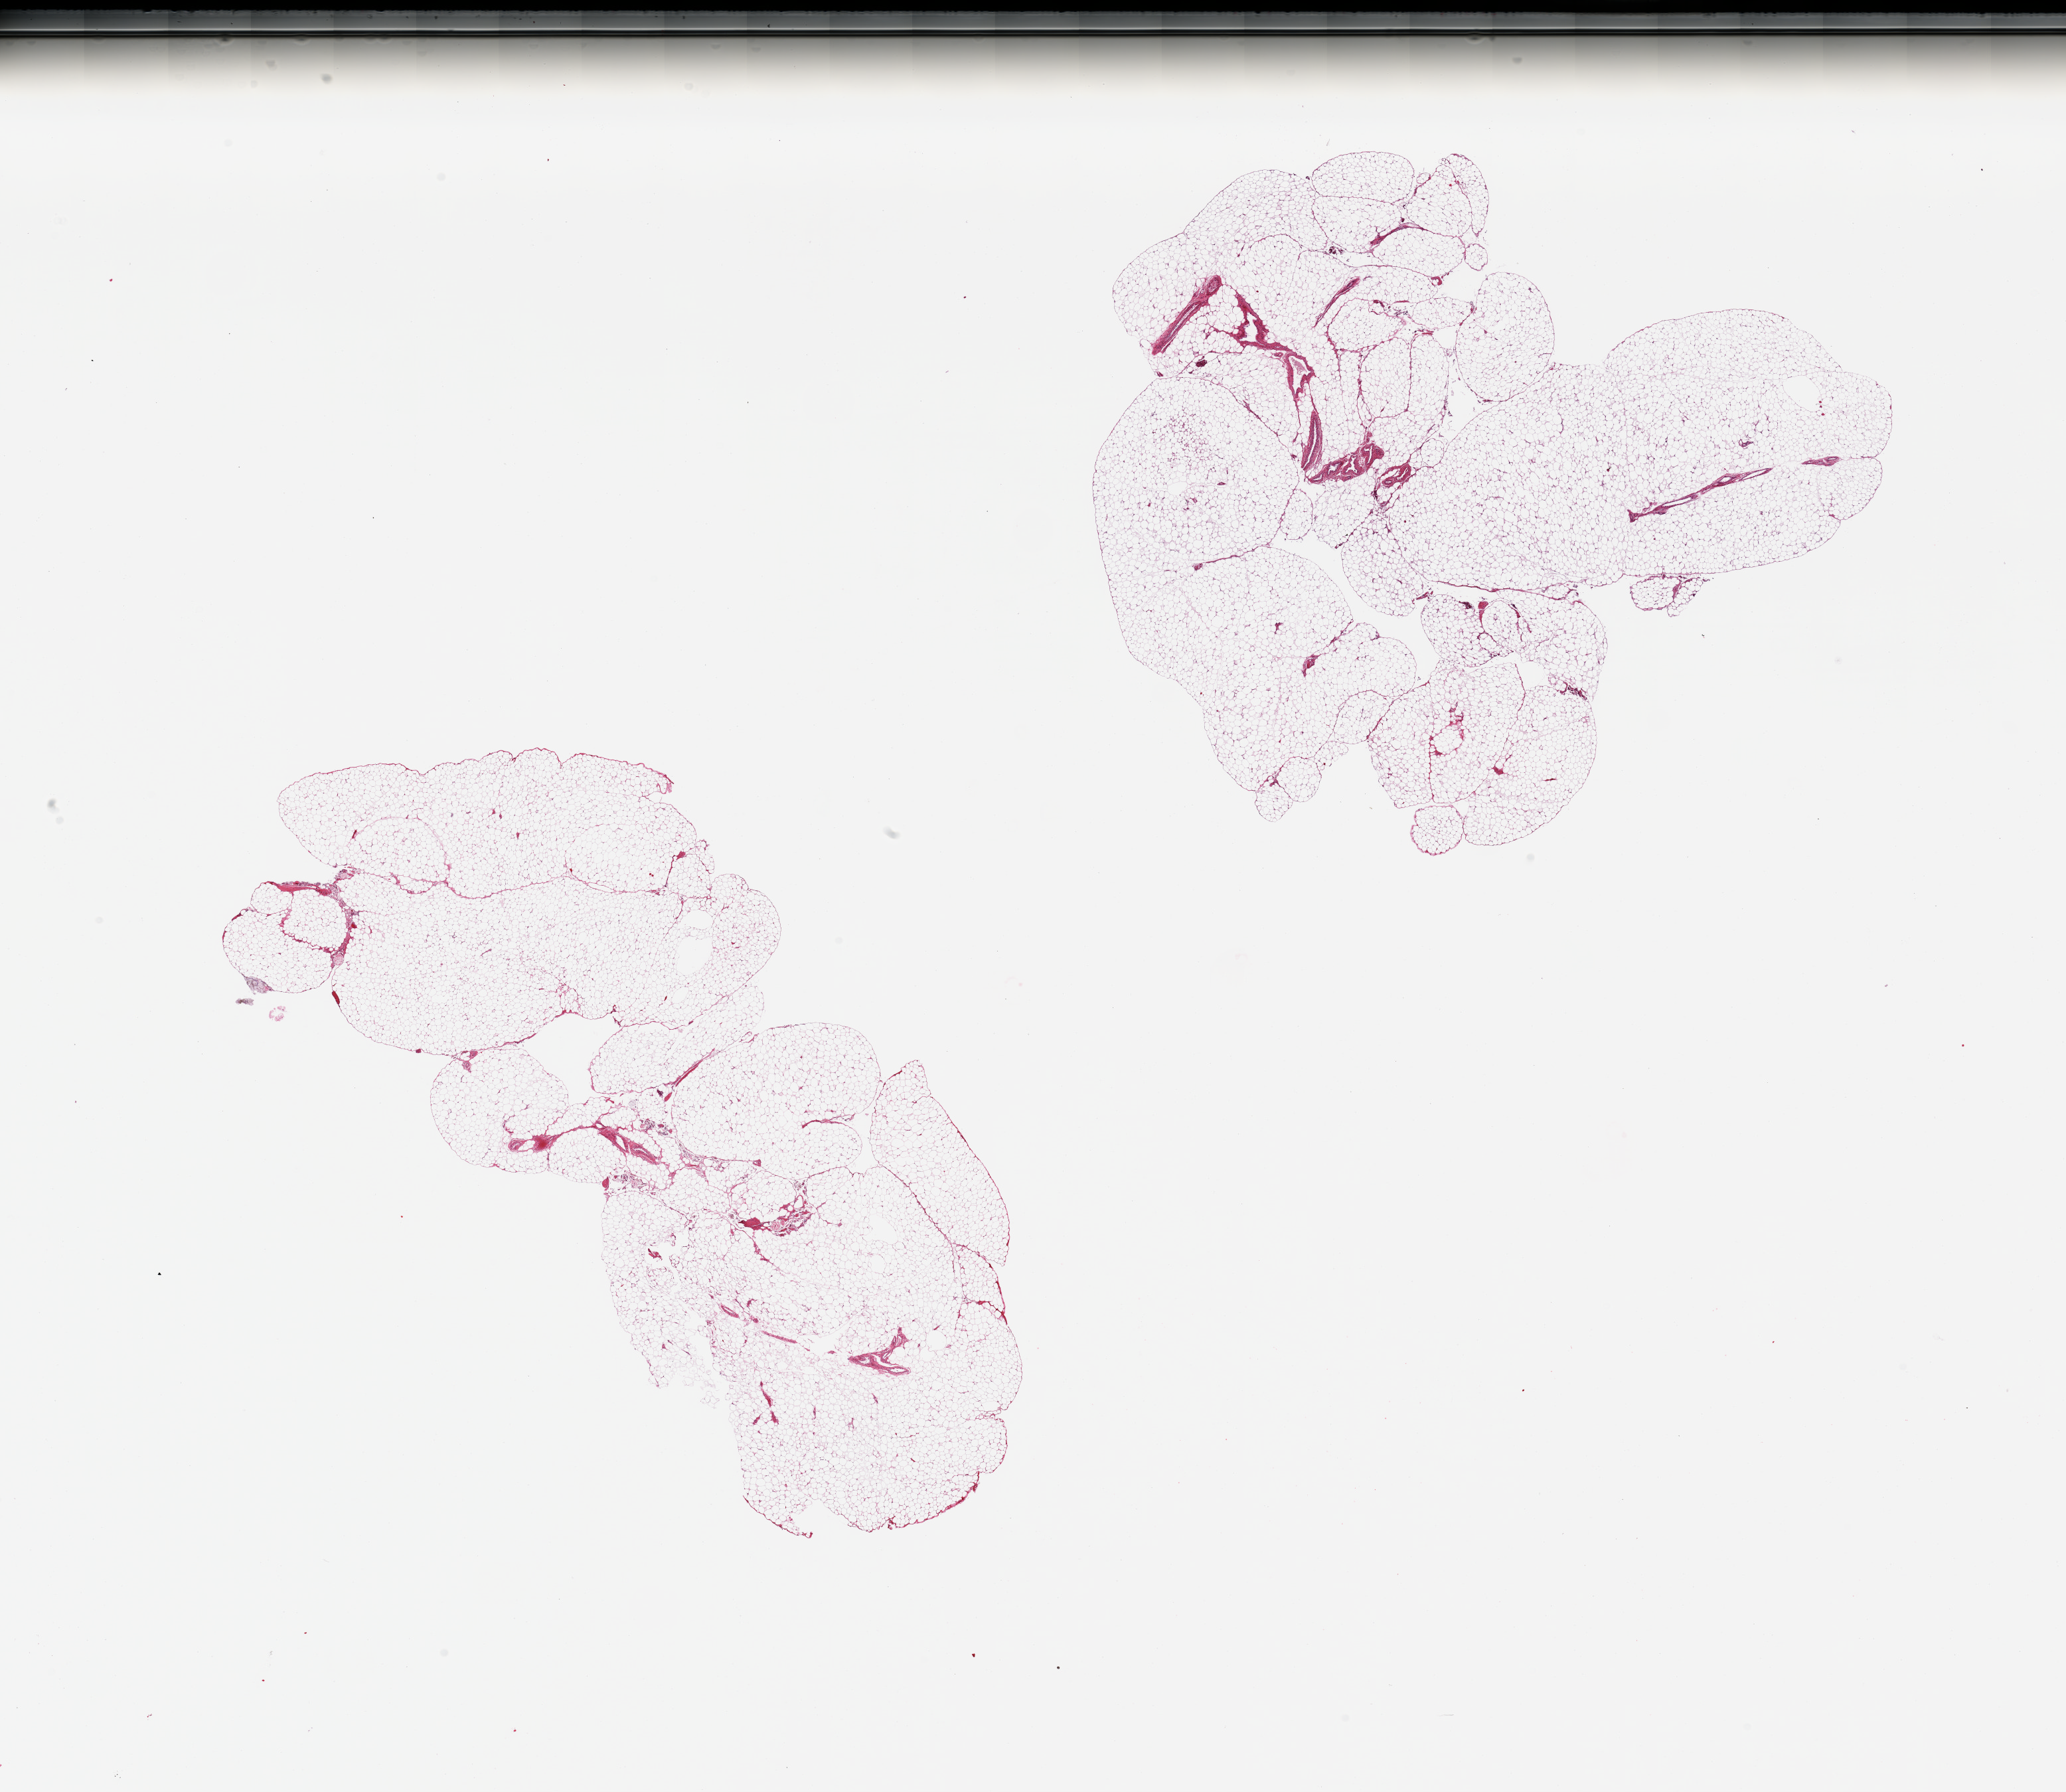
Digitized hematoxylin and eosin (H&E)-stained section — low-resolution overview of the scanned area, about 24.6 x 21.3 mm. PAXgene-fixed paraffin-embedded (PFPE) section. Sampled site (target tissue): omentum. Donor tissue sample. Male donor.
- reviewer comment on this tissue sample: 2 pieces; <2% fibrous content